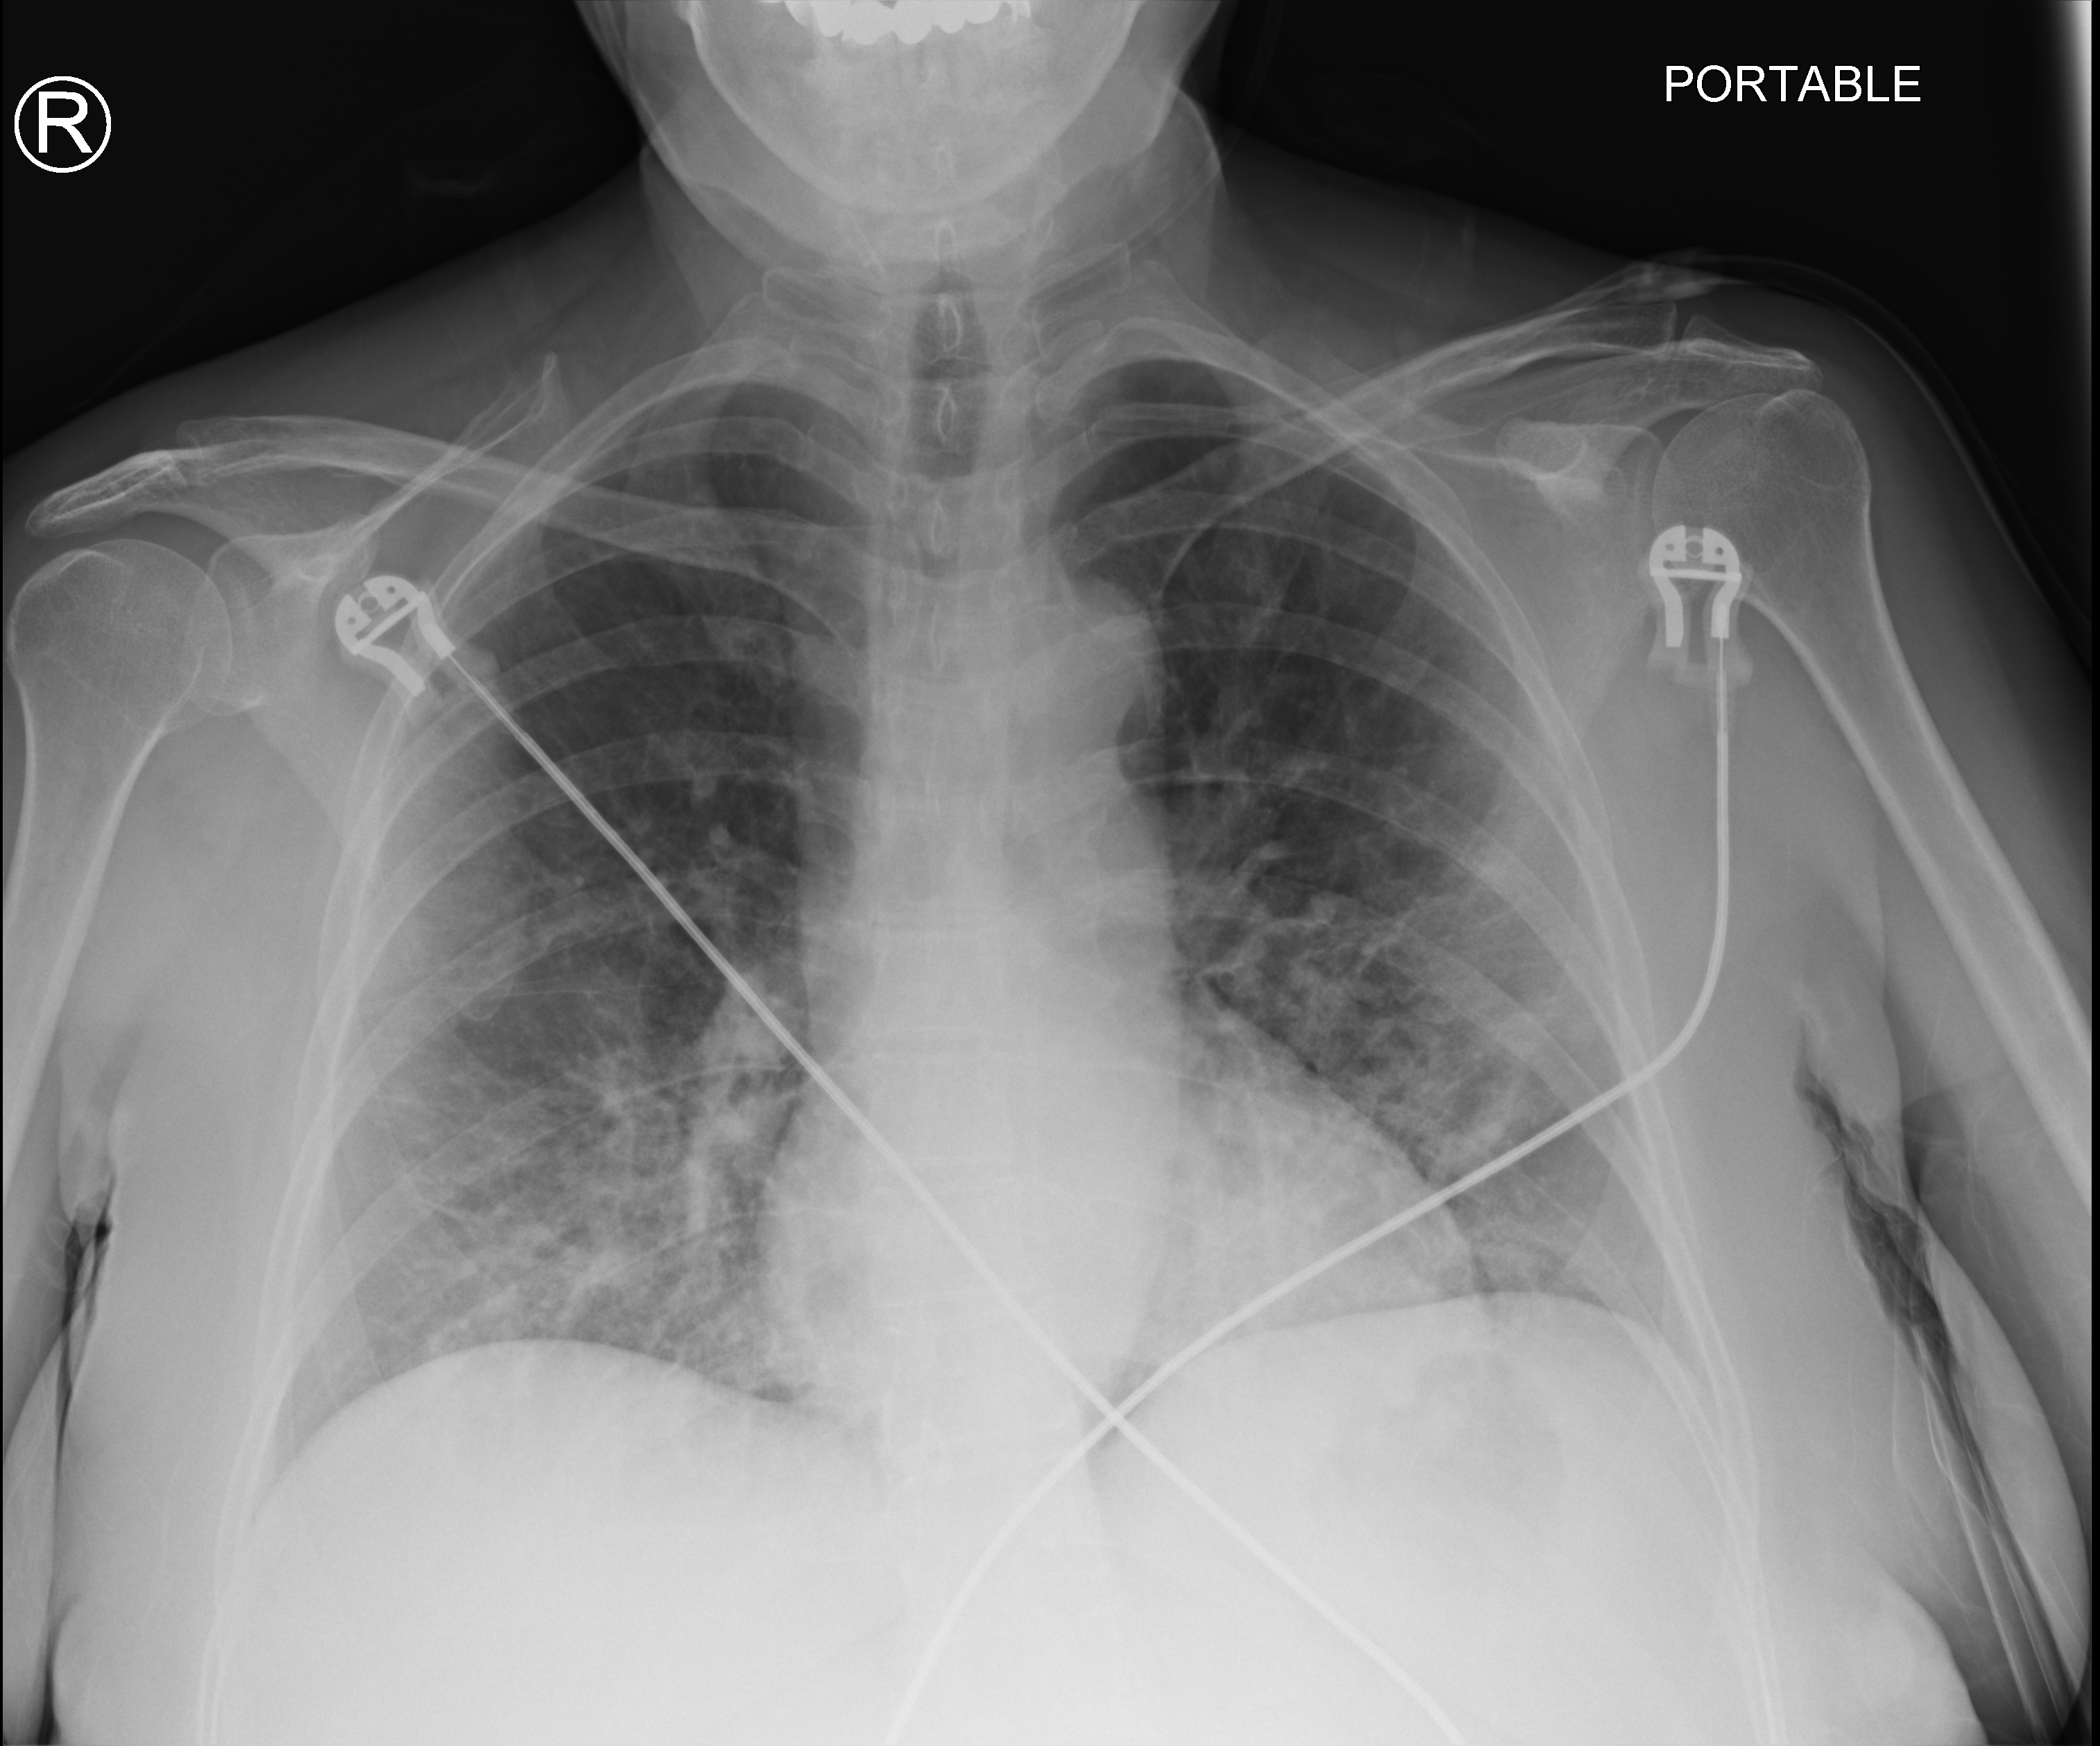
Bedside chest radiograph (computed radiography), anteroposterior (AP) projection. Female patient hospitalised with COVID-19, age 18–59 years.
From the hospital-stay record, not from the radiograph (when in the stay this image was taken is not recorded):
- mechanically ventilated during this hospital stay: no
- admitted to intensive care during this hospital stay: no